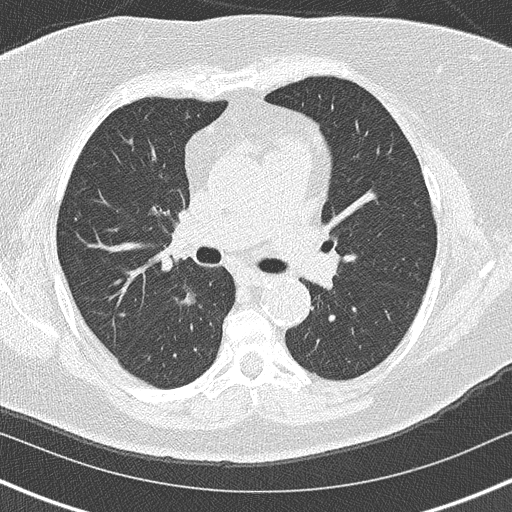
Low-dose screening chest CT, axial slice, second screening round (one year after baseline), lung window (W 1500 / L -600 HU), 2 mm slice thickness, lung (sharp) reconstruction kernel (B50f), slice 59 of 152 in the series. Female participant, aged 60 years at enrolment. Former smoker at enrolment.
Lesion marked by an expert reader, bounding box [x1, y1, x2, y2] px = [148, 270, 218, 329]. Screening reader's record for this exam (one nodule recorded; not confirmed to be the boxed lesion): non-calcified nodule or mass ≥4 mm, right lower lobe, 20 × 19 mm, soft tissue attenuation, pre-existing on the prior screen: yes; interval growth: yes. Official screen result: positive, other. Participant outcome: lung cancer diagnosed 139 days after this screen — bronchiolo-alveolar carcinoma, non-mucinous, right lower lobe, stage IA (AJCC 6th edition), 15 mm at pathology.